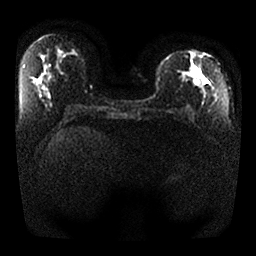
Breast MRI, one axial slice; slice 12 of 25 in the series (ordered by position); diffusion-weighted series; image 2 of 4 stored at this slice position (different b-values; order by instance number); 1.5 T; 4 mm slice thickness; 256 × 256 image matrix. Female patient.
Structures marked on this image (manually delineated by an expert):
- tumour on diffusion-weighted imaging: box from (x=179, y=70) to (x=202, y=87) px